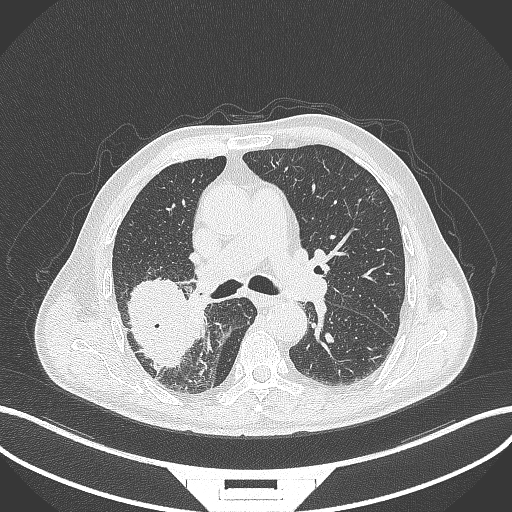
Chest CT, one axial slice; slice 249 of 429 in the series (ordered by position); reconstruction kernel B70f; 120 kVp; lung window (W 1500 / L -600 HU); 1 mm slice thickness; 512 × 512 image matrix, field of view 400 × 400 mm. Patient: male, 72 years. Case-level facts recorded for this patient, not image findings: clinical TNM (as recorded): T3 N2 M0.
Structures marked on this image (rectangle marked by the reading radiologist):
- lung tumour (recorded histology: adenocarcinoma): bounding box (x1, y1, x2, y2) in pixels: (121, 275, 194, 370)